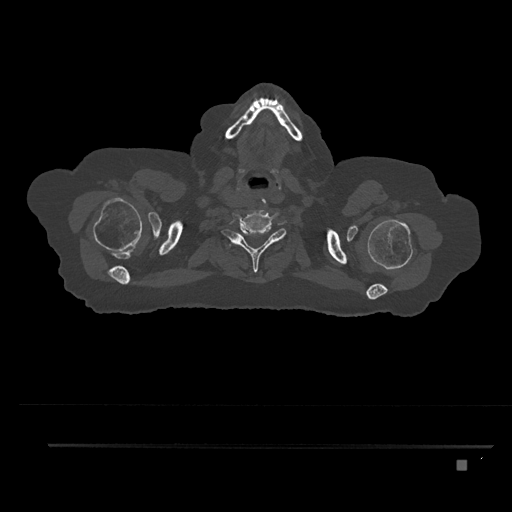
CT including the spine, one axial slice; reconstruction kernel Br40s/3; 120 kVp; bone window (W 1800 / L 400 HU); 0.5 mm slice thickness; 512 × 512 image matrix, field of view 437 × 437 mm. Patient: female, 76 years. Case-level facts recorded for this patient, not image findings: primary cancer: lung; vertebrae with lytic lesions (as recorded): T11, L3.
Outlined on this slice (semi-automatic segmentation, software-assisted and operator-edited):
- T1 vertebra: bounding box (x1, y1, x2, y2) in pixels: (231, 240, 250, 254)